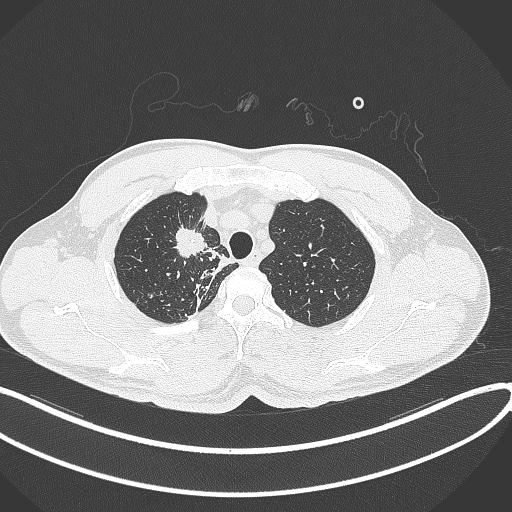
Chest CT, one axial slice; slice 316 of 391 in the series (ordered by position); 120 kVp; lung window (W 1500 / L -600 HU); 1 mm slice thickness; 512 × 512 image matrix, field of view 400 × 400 mm. Male patient, age 48 years. From the clinical record (not read from this slice): clinical TNM (as recorded): T1c N1 M1.
Annotated regions visible in this slice (bounding box drawn by a radiologist):
- lung tumour (recorded histology: adenocarcinoma): bounding box (x1, y1, x2, y2) in pixels: (172, 224, 212, 261)